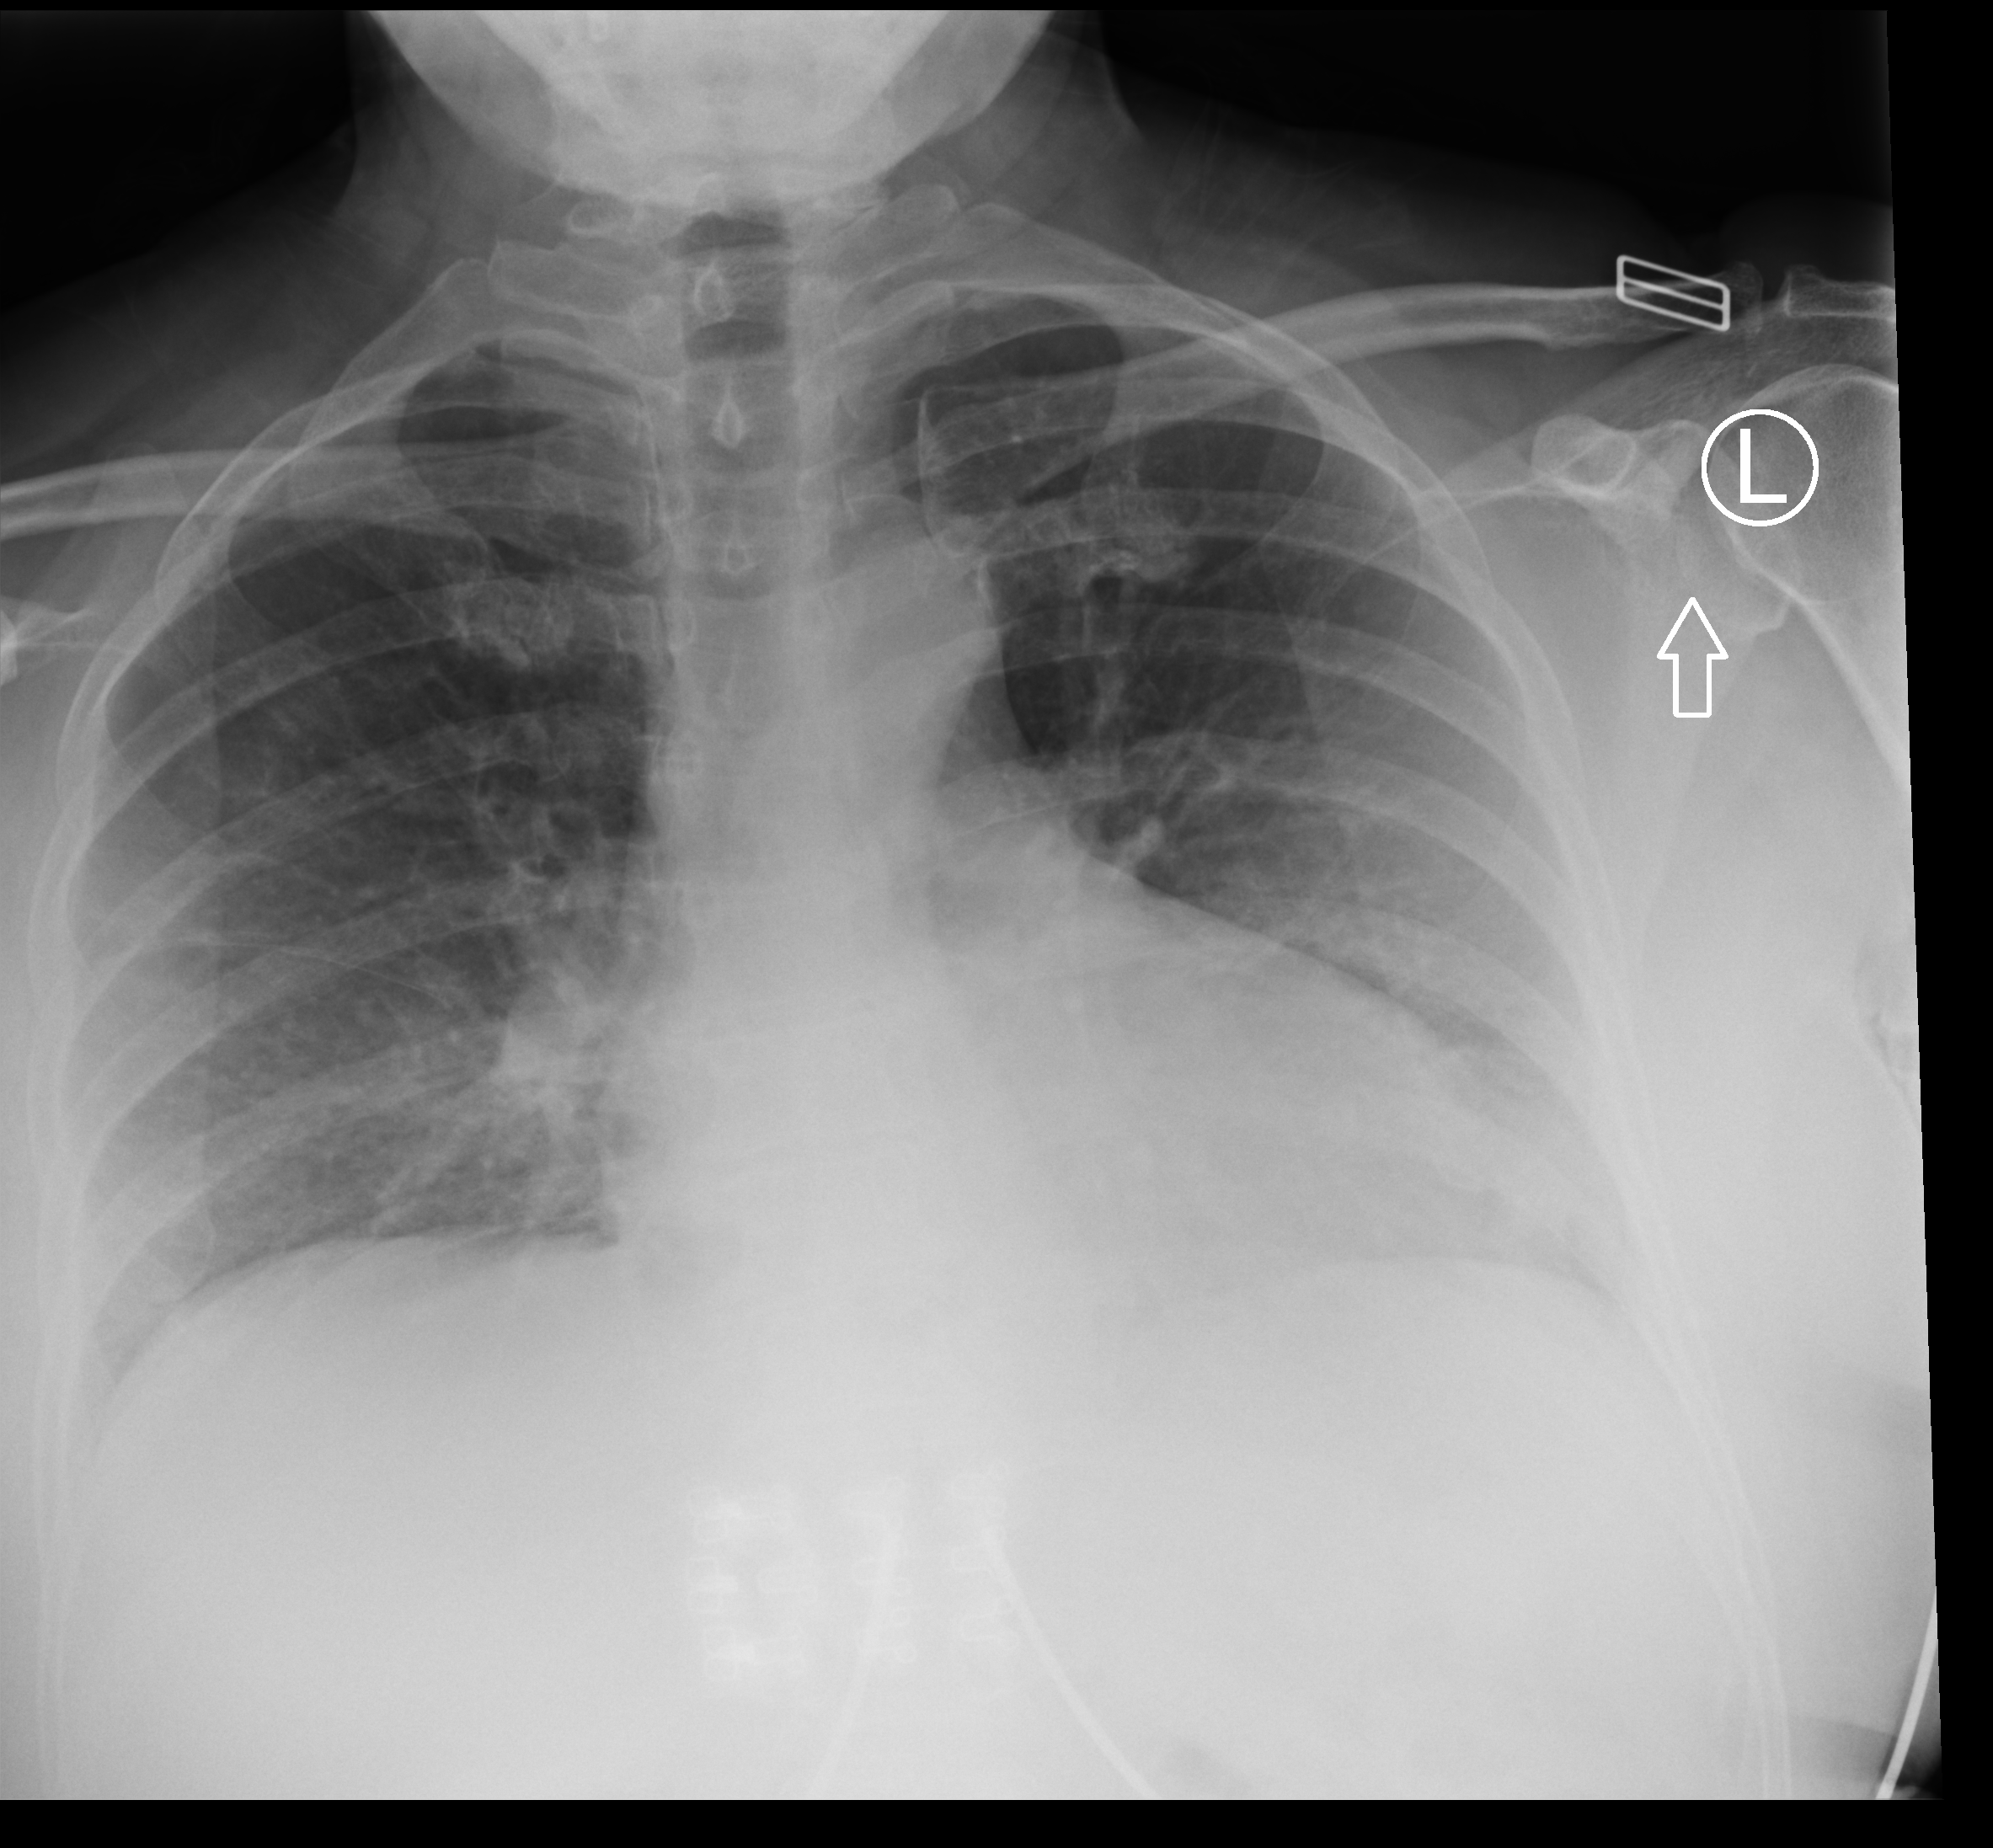
Chest X-ray (portable). Female patient hospitalised with COVID-19, age 60–74 years.
Hospital-stay facts (about this admission, not read from this image; timing relative to this image not recorded):
- admitted to intensive care during this hospital stay: no